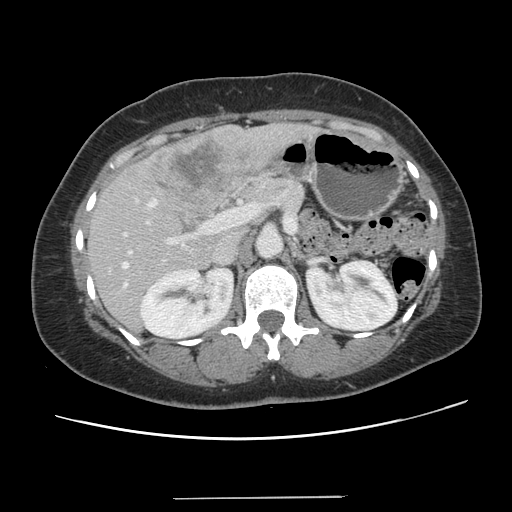
Contrast-enhanced abdominal CT, one axial slice; slice 69 of 141 in the series (ordered by position); 120 kVp; intravenous contrast given; soft-tissue window (W 400 / L 40 HU); 2.5 mm slice thickness; 512 × 512 image matrix. Female patient, age 53 years. Case-level facts recorded for this patient, not image findings: diagnosis: colorectal cancer liver metastases, imaged before liver resection; multiple liver metastases: no; largest metastasis: 14.5 cm; disease in both lobes: yes.
Annotated regions visible in this slice (expert manual segmentation):
- hepatic veins: bounding box <122,250,131,288> (left, top, right, bottom; pixels)
- liver: <89,124,309,330>
- planned liver remnant (the part of the liver to remain after resection): <89,209,248,330>
- portal vein (with intrahepatic branches): <124,199,226,243>
- liver metastasis: <146,136,250,207>